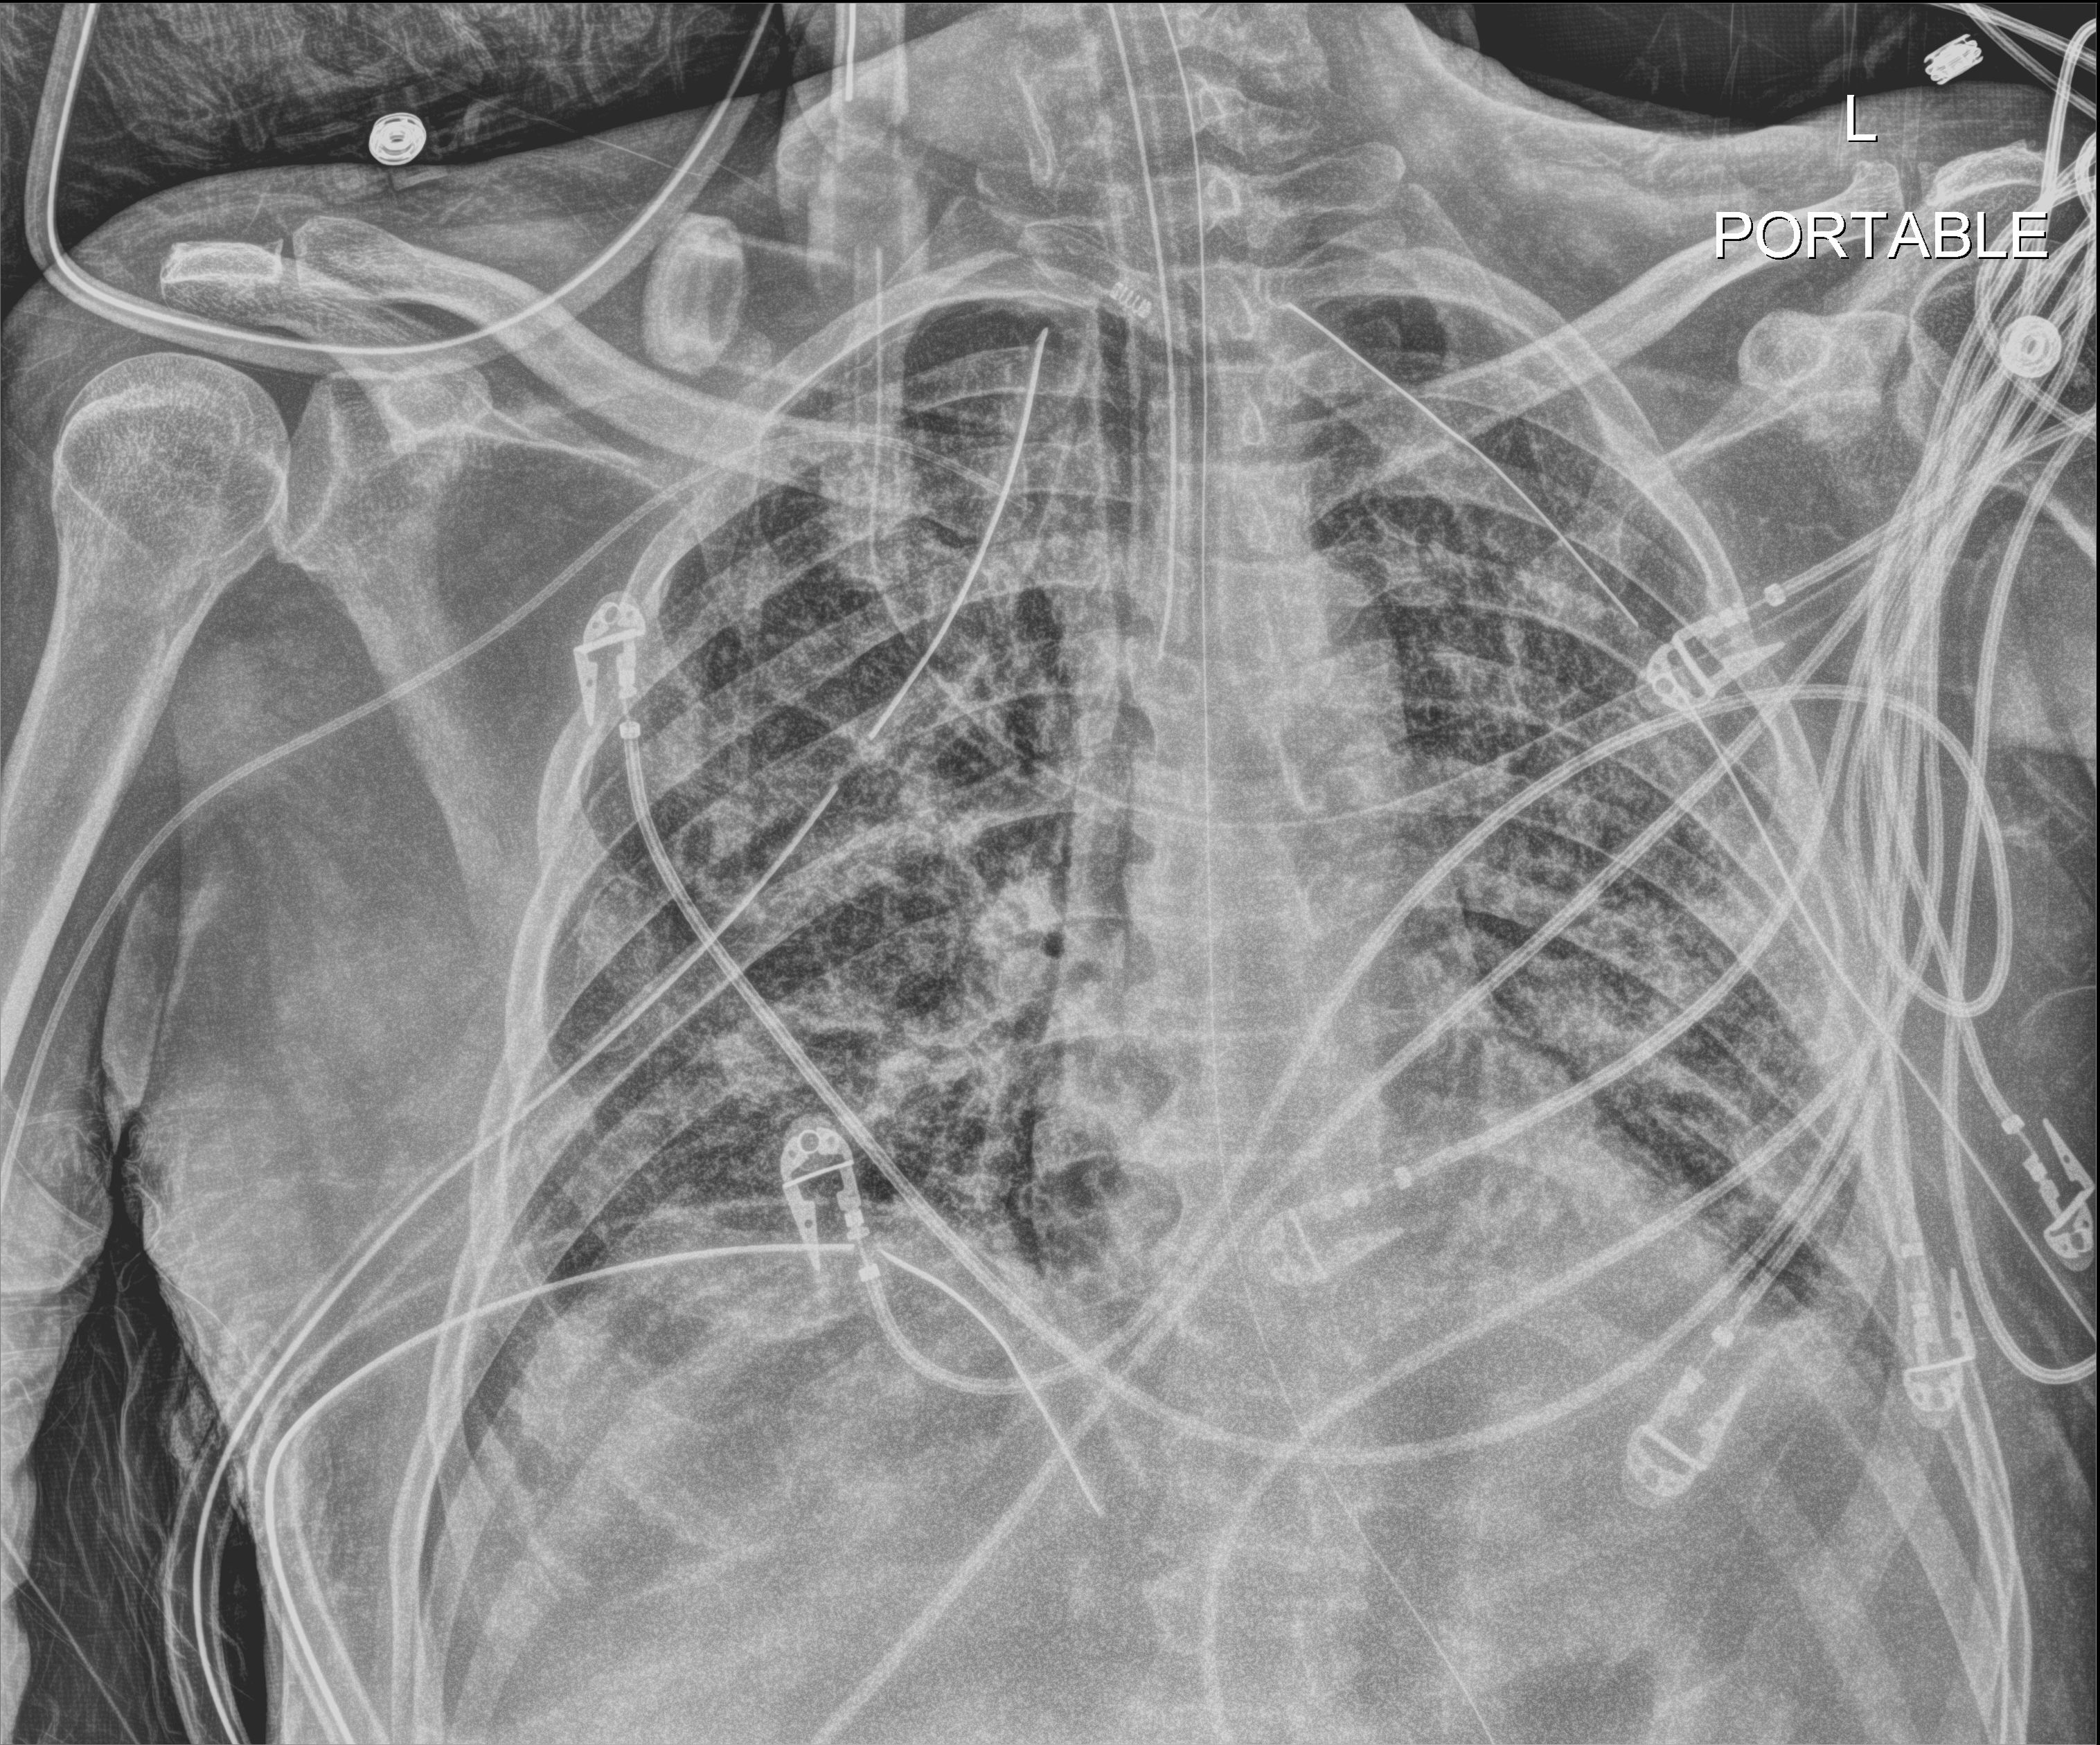
Portable chest radiograph; anteroposterior (AP) projection. Patient hospitalised with COVID-19; male, aged 18–59 years.
Admission-level facts for this patient (not findings on this image; timing relative to this image not recorded):
- mechanically ventilated during this hospital stay: yes